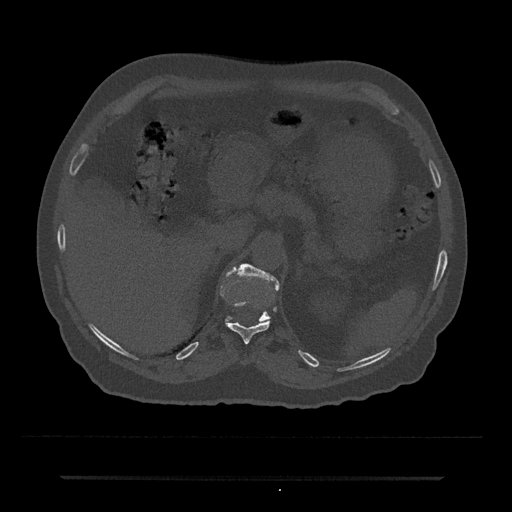
CT including the spine, one axial slice; position 167 of 797 along the scan axis; reconstruction kernel Br40s/3; 120 kVp; bone window (W 1800 / L 400 HU); 512 × 512 image matrix, field of view 437 × 437 mm. Male patient, age 69 years. From the clinical record (not read from this slice): primary cancer: prostate.
Annotated regions visible in this slice (semi-automatically segmented with operator editing):
- T11 vertebra: box from (x=227, y=301) to (x=270, y=344) px
- T12 vertebra: (x=226, y=264)–(x=280, y=322)